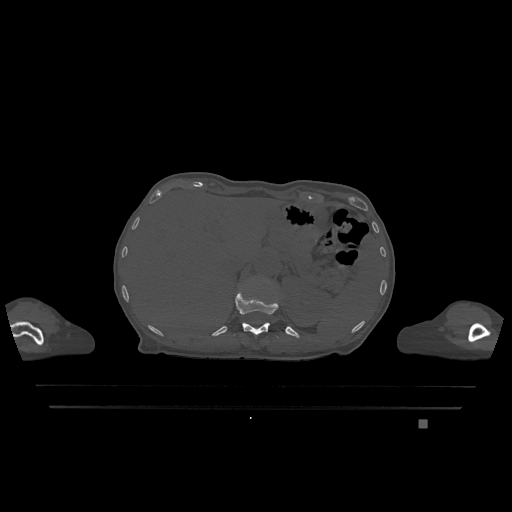
CT including the spine, one axial slice. Slice 526 of 1317 in the series (ordered by position). Bone window (W 1800 / L 400 HU). 0.5 mm slice thickness. 512 × 512 image matrix. Female patient, age 74 years. From the clinical record (not read from this slice): primary cancer: lung; vertebrae with lytic lesions (as recorded): T1, T4, T5, T6, L4, L5.
Outlined on this slice (semi-automatic segmentation, software-assisted and operator-edited):
- T12 vertebra: box from (x=234, y=289) to (x=279, y=338) px